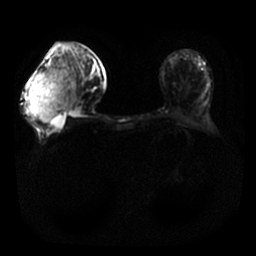
Breast MRI, one axial slice. Slice 2 of 25 in the series (ordered by position). Diffusion-weighted series; image 2 of 4 stored at this slice position (different b-values; order by instance number). 1.5 T. 4 mm slice thickness. 256 × 256 image matrix, field of view 340 × 340 mm. Female patient.
Structures marked on this image (outlined manually by an expert reader):
- tumour on diffusion-weighted imaging: bounding box [x1, y1, x2, y2] px = [29, 68, 76, 123]